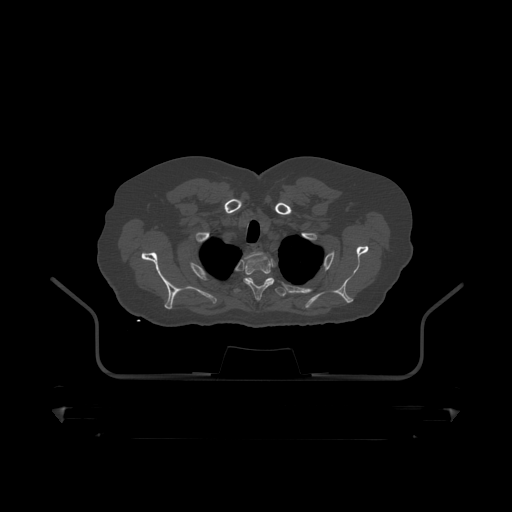
CT including the spine, one axial slice. Position 372 of 390 along the scan axis. Reconstruction kernel STANDARD. 120 kVp. Bone window (W 1800 / L 400 HU). 1.25 mm slice thickness. 512 × 512 image matrix, field of view 650 × 650 mm. Male patient, age 60 years. Case-level facts recorded for this patient, not image findings: primary cancer: prostate.
Annotated regions visible in this slice (semi-automatic segmentation, software-assisted and operator-edited):
- T1 vertebra: bounding box (x1, y1, x2, y2) in pixels: (241, 252, 261, 268)
- T2 vertebra: (244, 256, 275, 300)
- T3 vertebra: (233, 278, 287, 297)